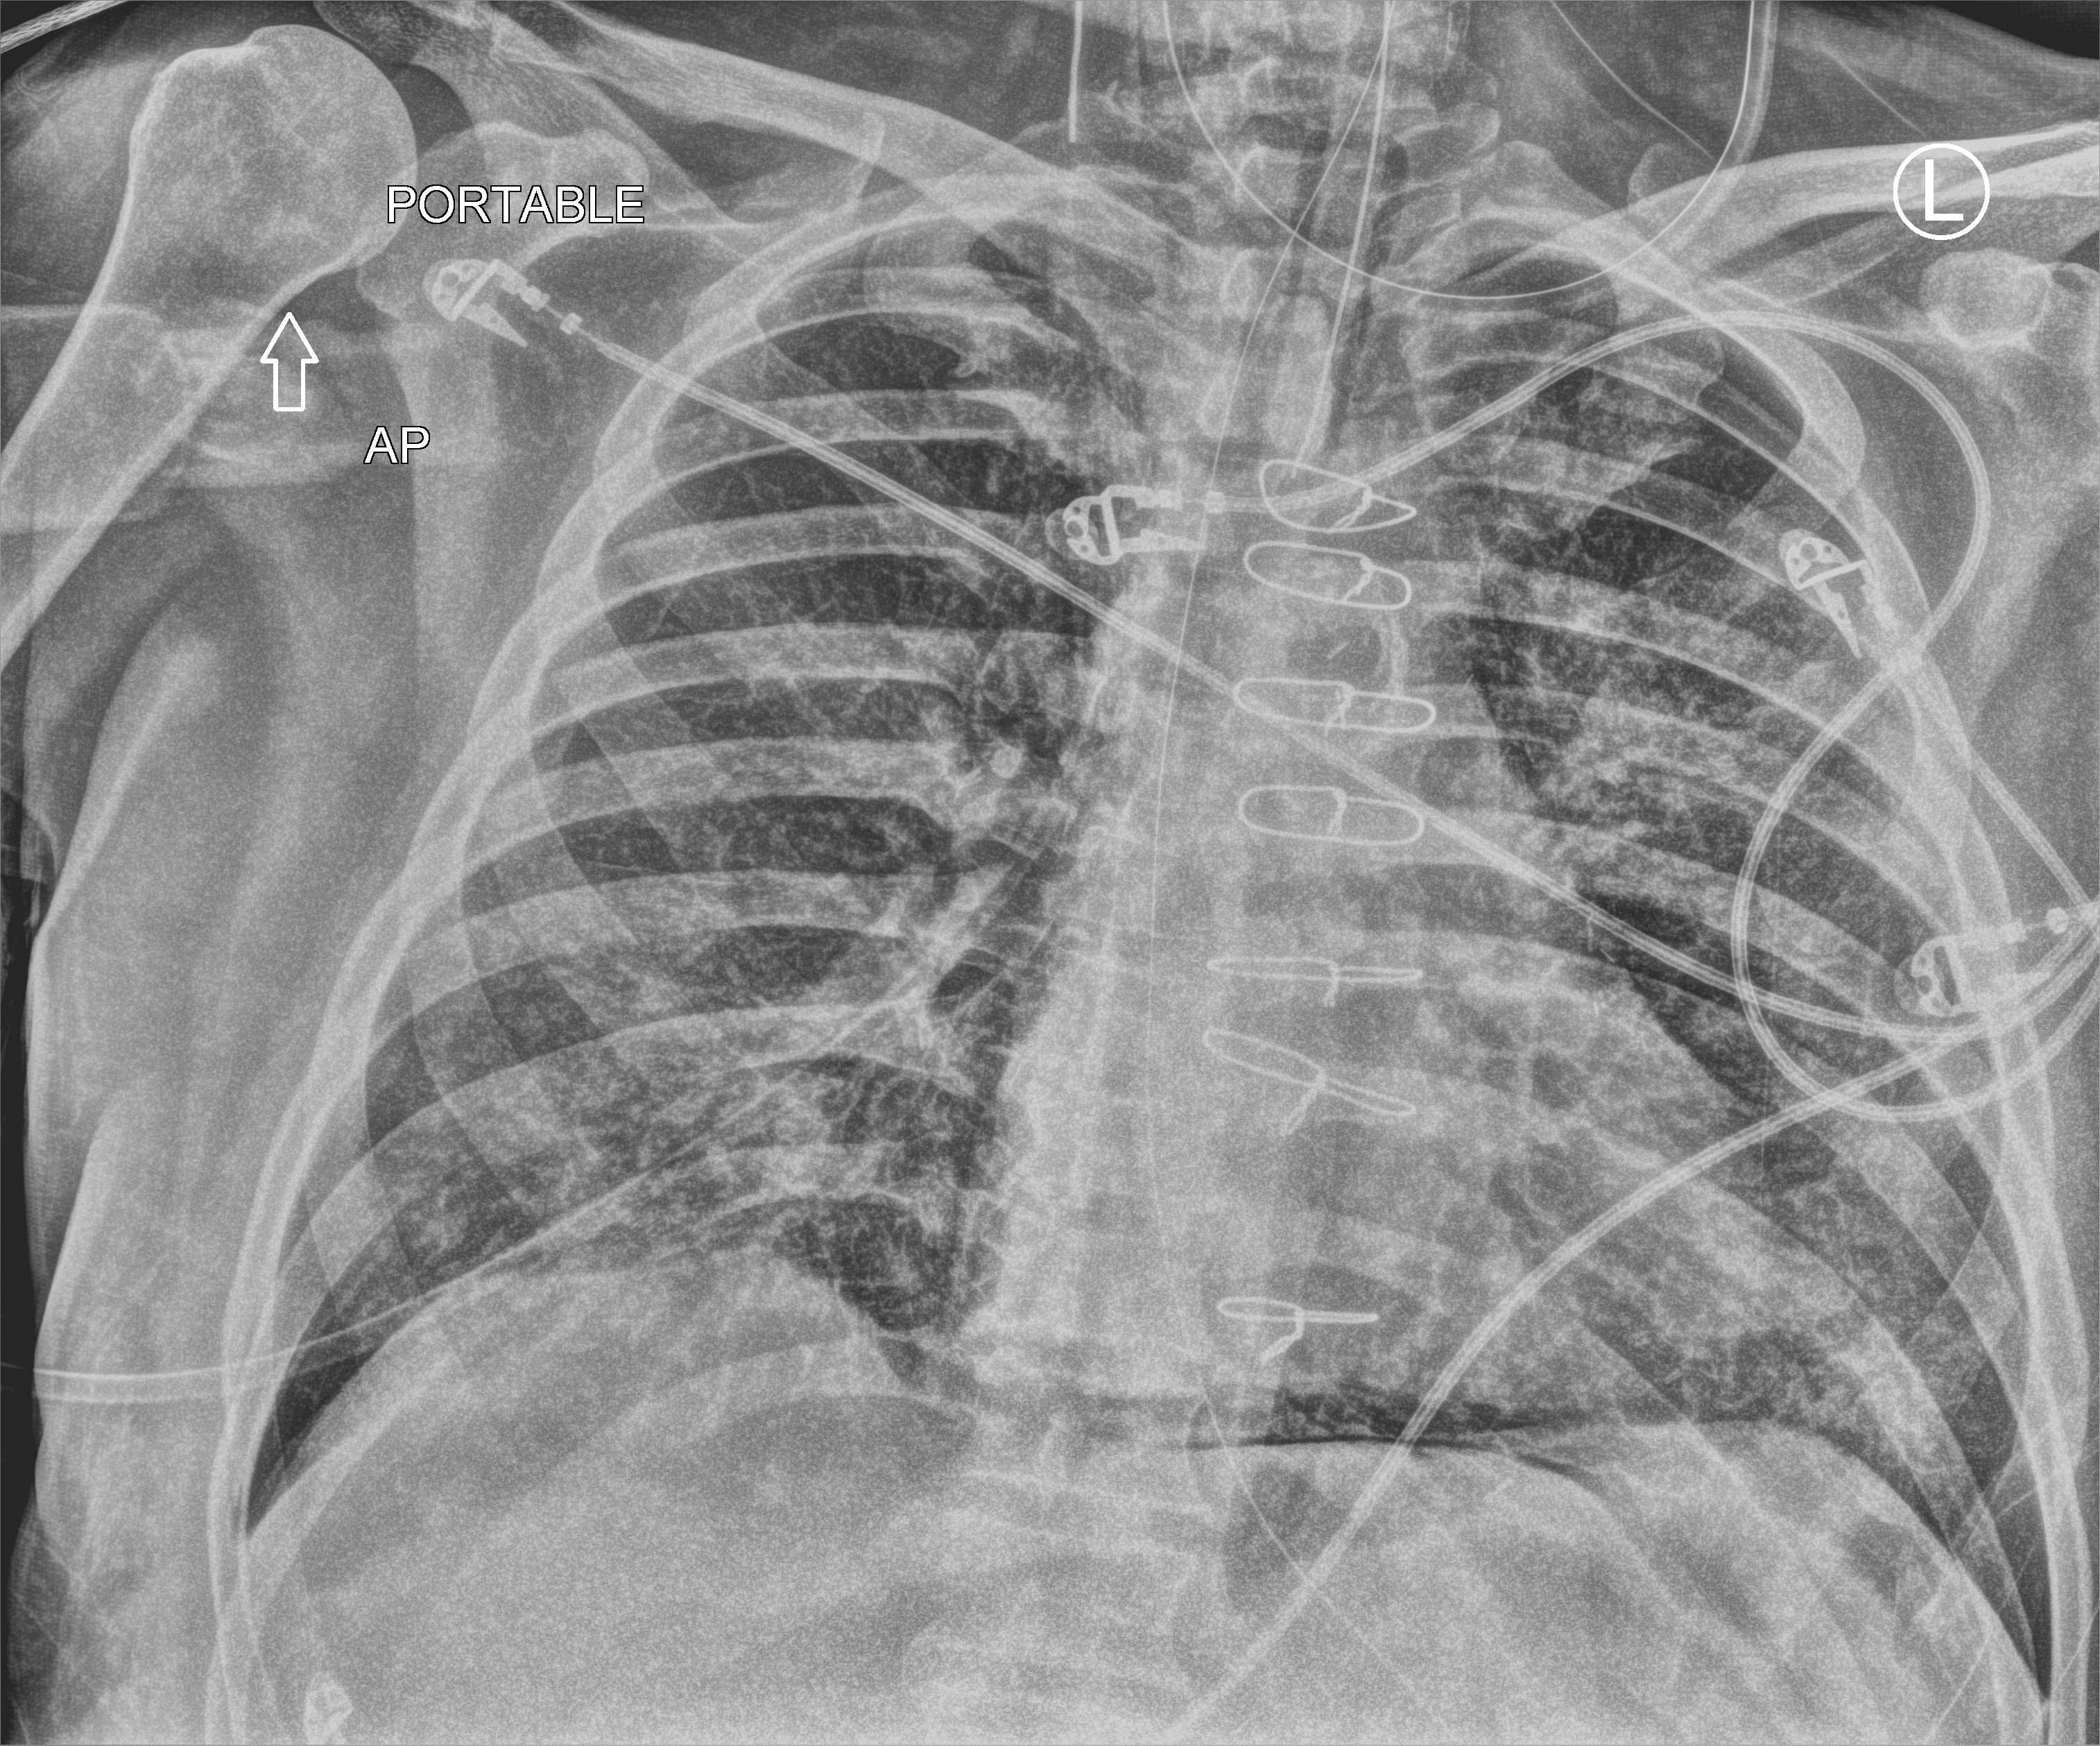
Bedside chest radiograph (computed radiography), anteroposterior (AP) projection. Patient hospitalised with COVID-19; male, aged 60–74 years.
From the hospital-stay record, not from the radiograph (when in the stay this image was taken is not recorded): admitted to intensive care during this hospital stay: yes; mechanically ventilated during this hospital stay: yes.